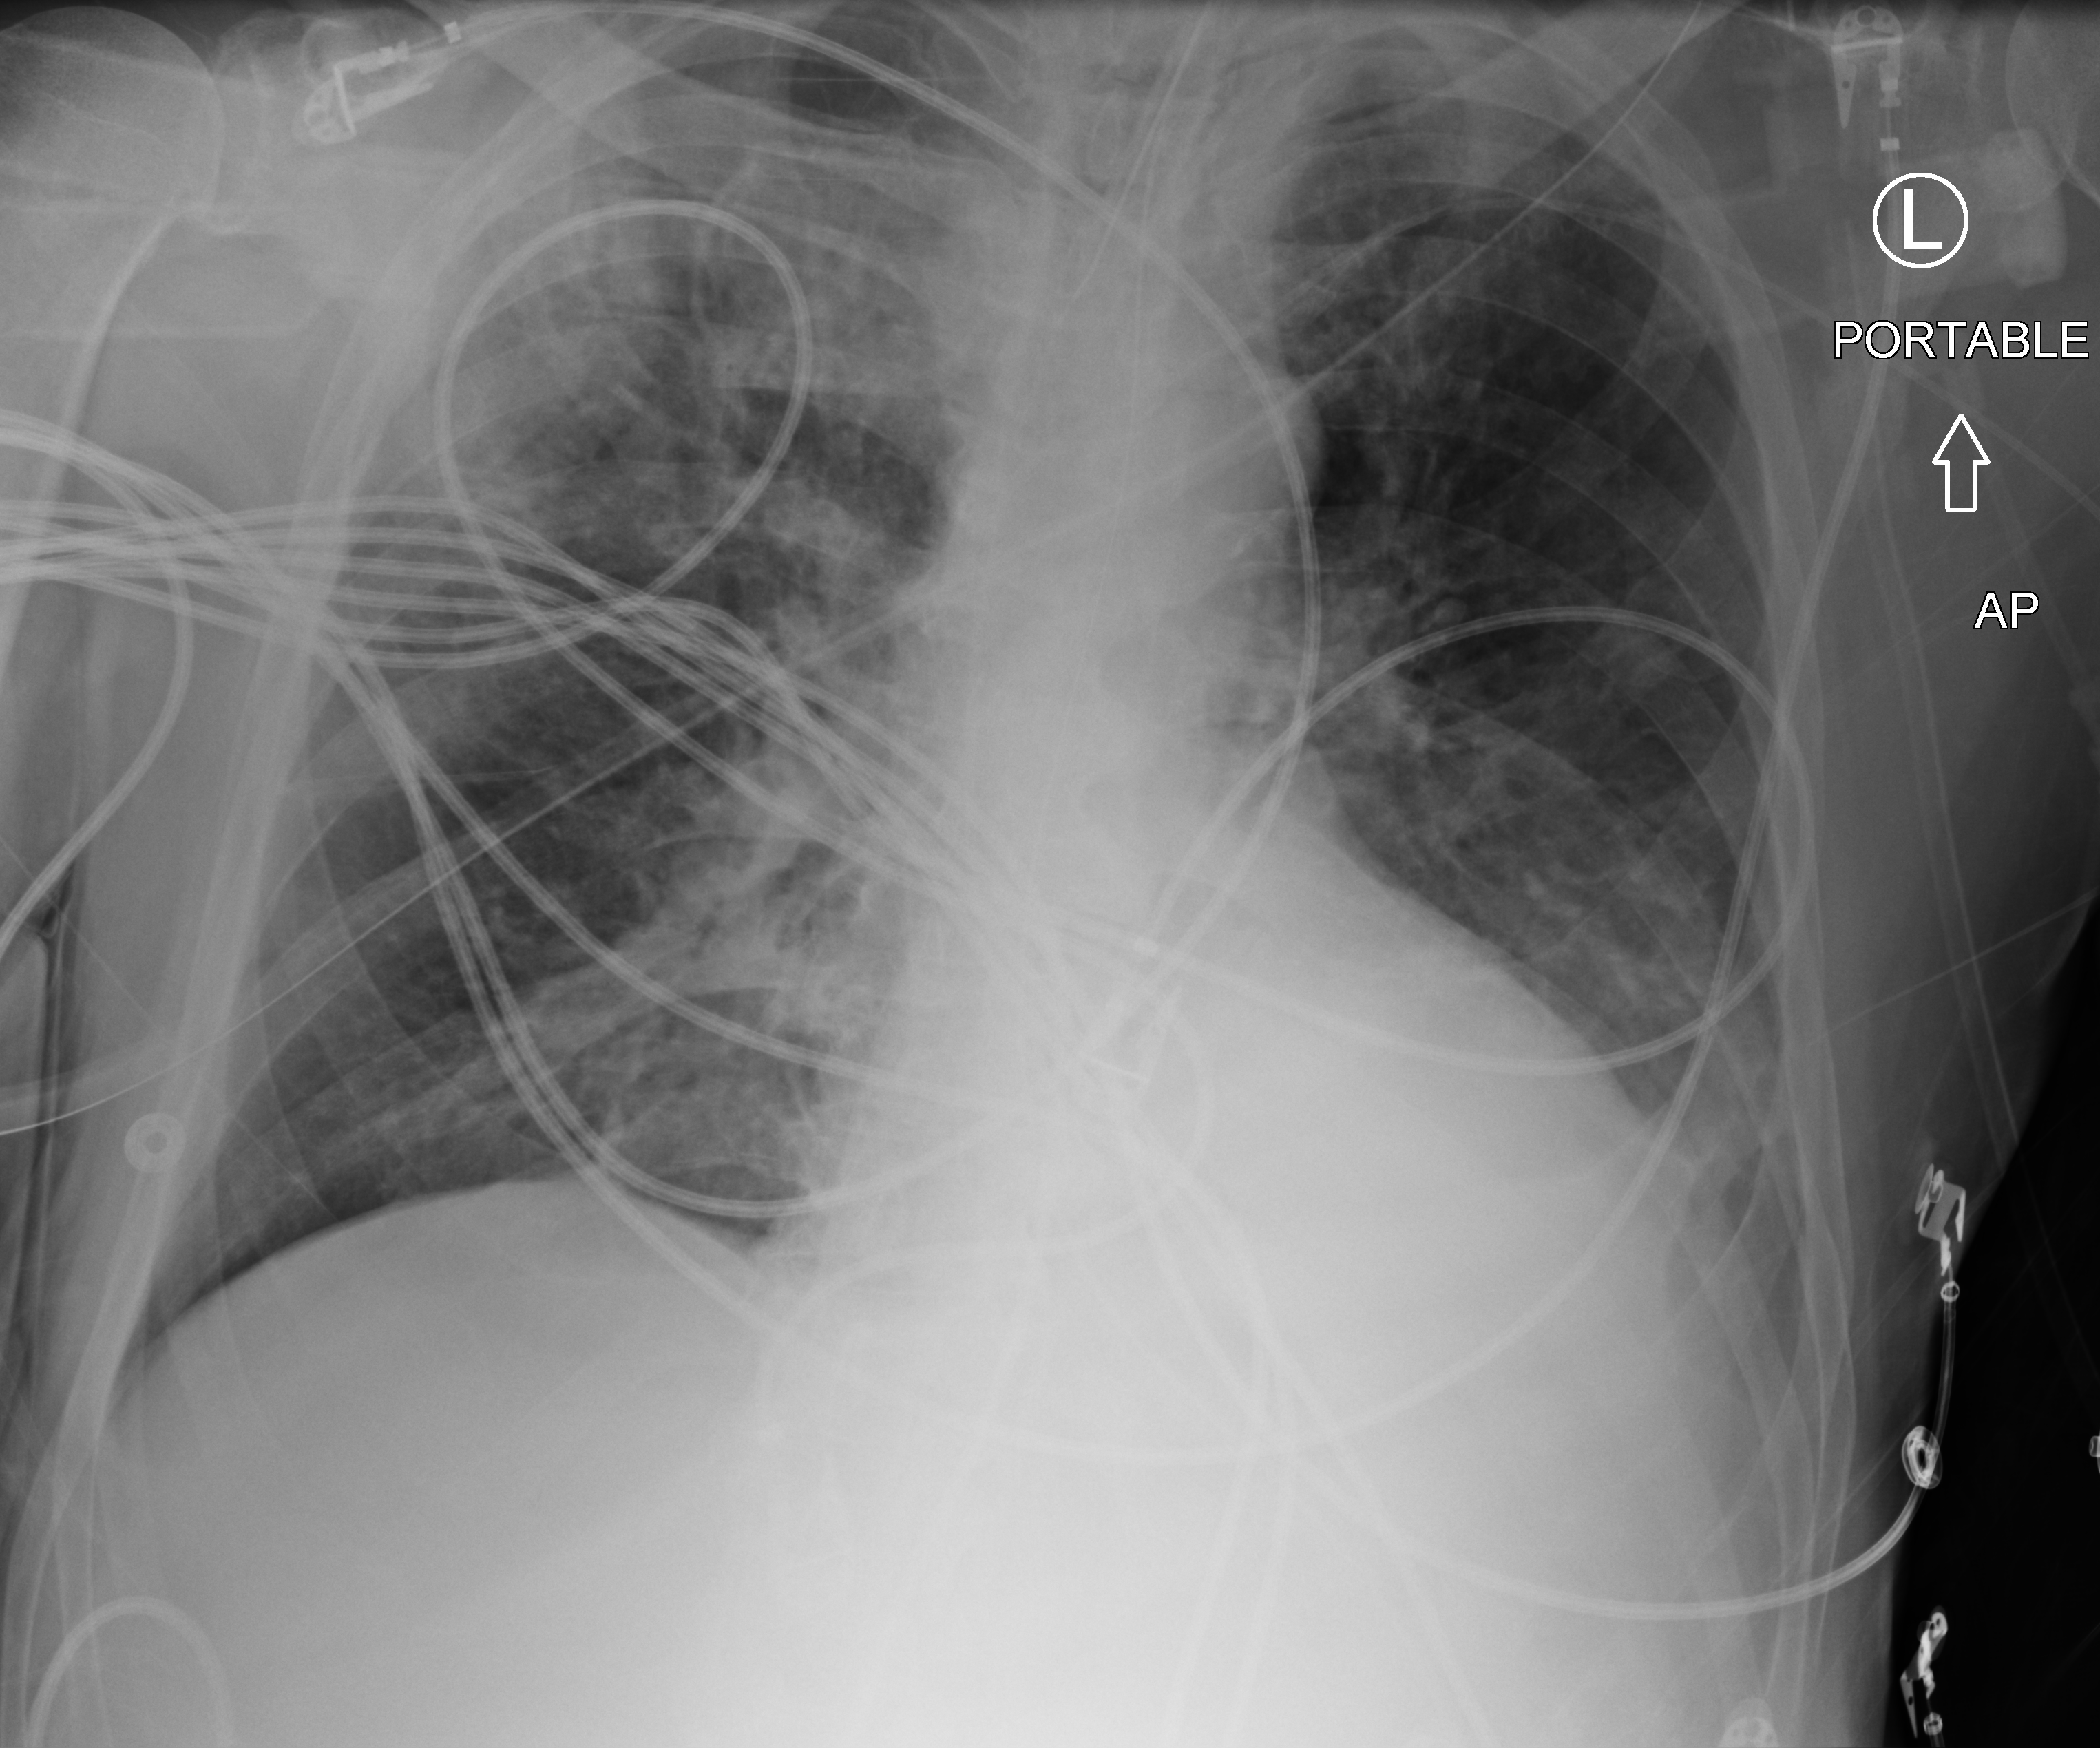
Portable chest radiograph, anteroposterior (AP) projection. Patient hospitalised with COVID-19; male, aged 60–74 years.
Hospital-stay facts (about this admission, not read from this image; timing relative to this image not recorded): admitted to intensive care during this hospital stay: yes; mechanically ventilated during this hospital stay: yes.